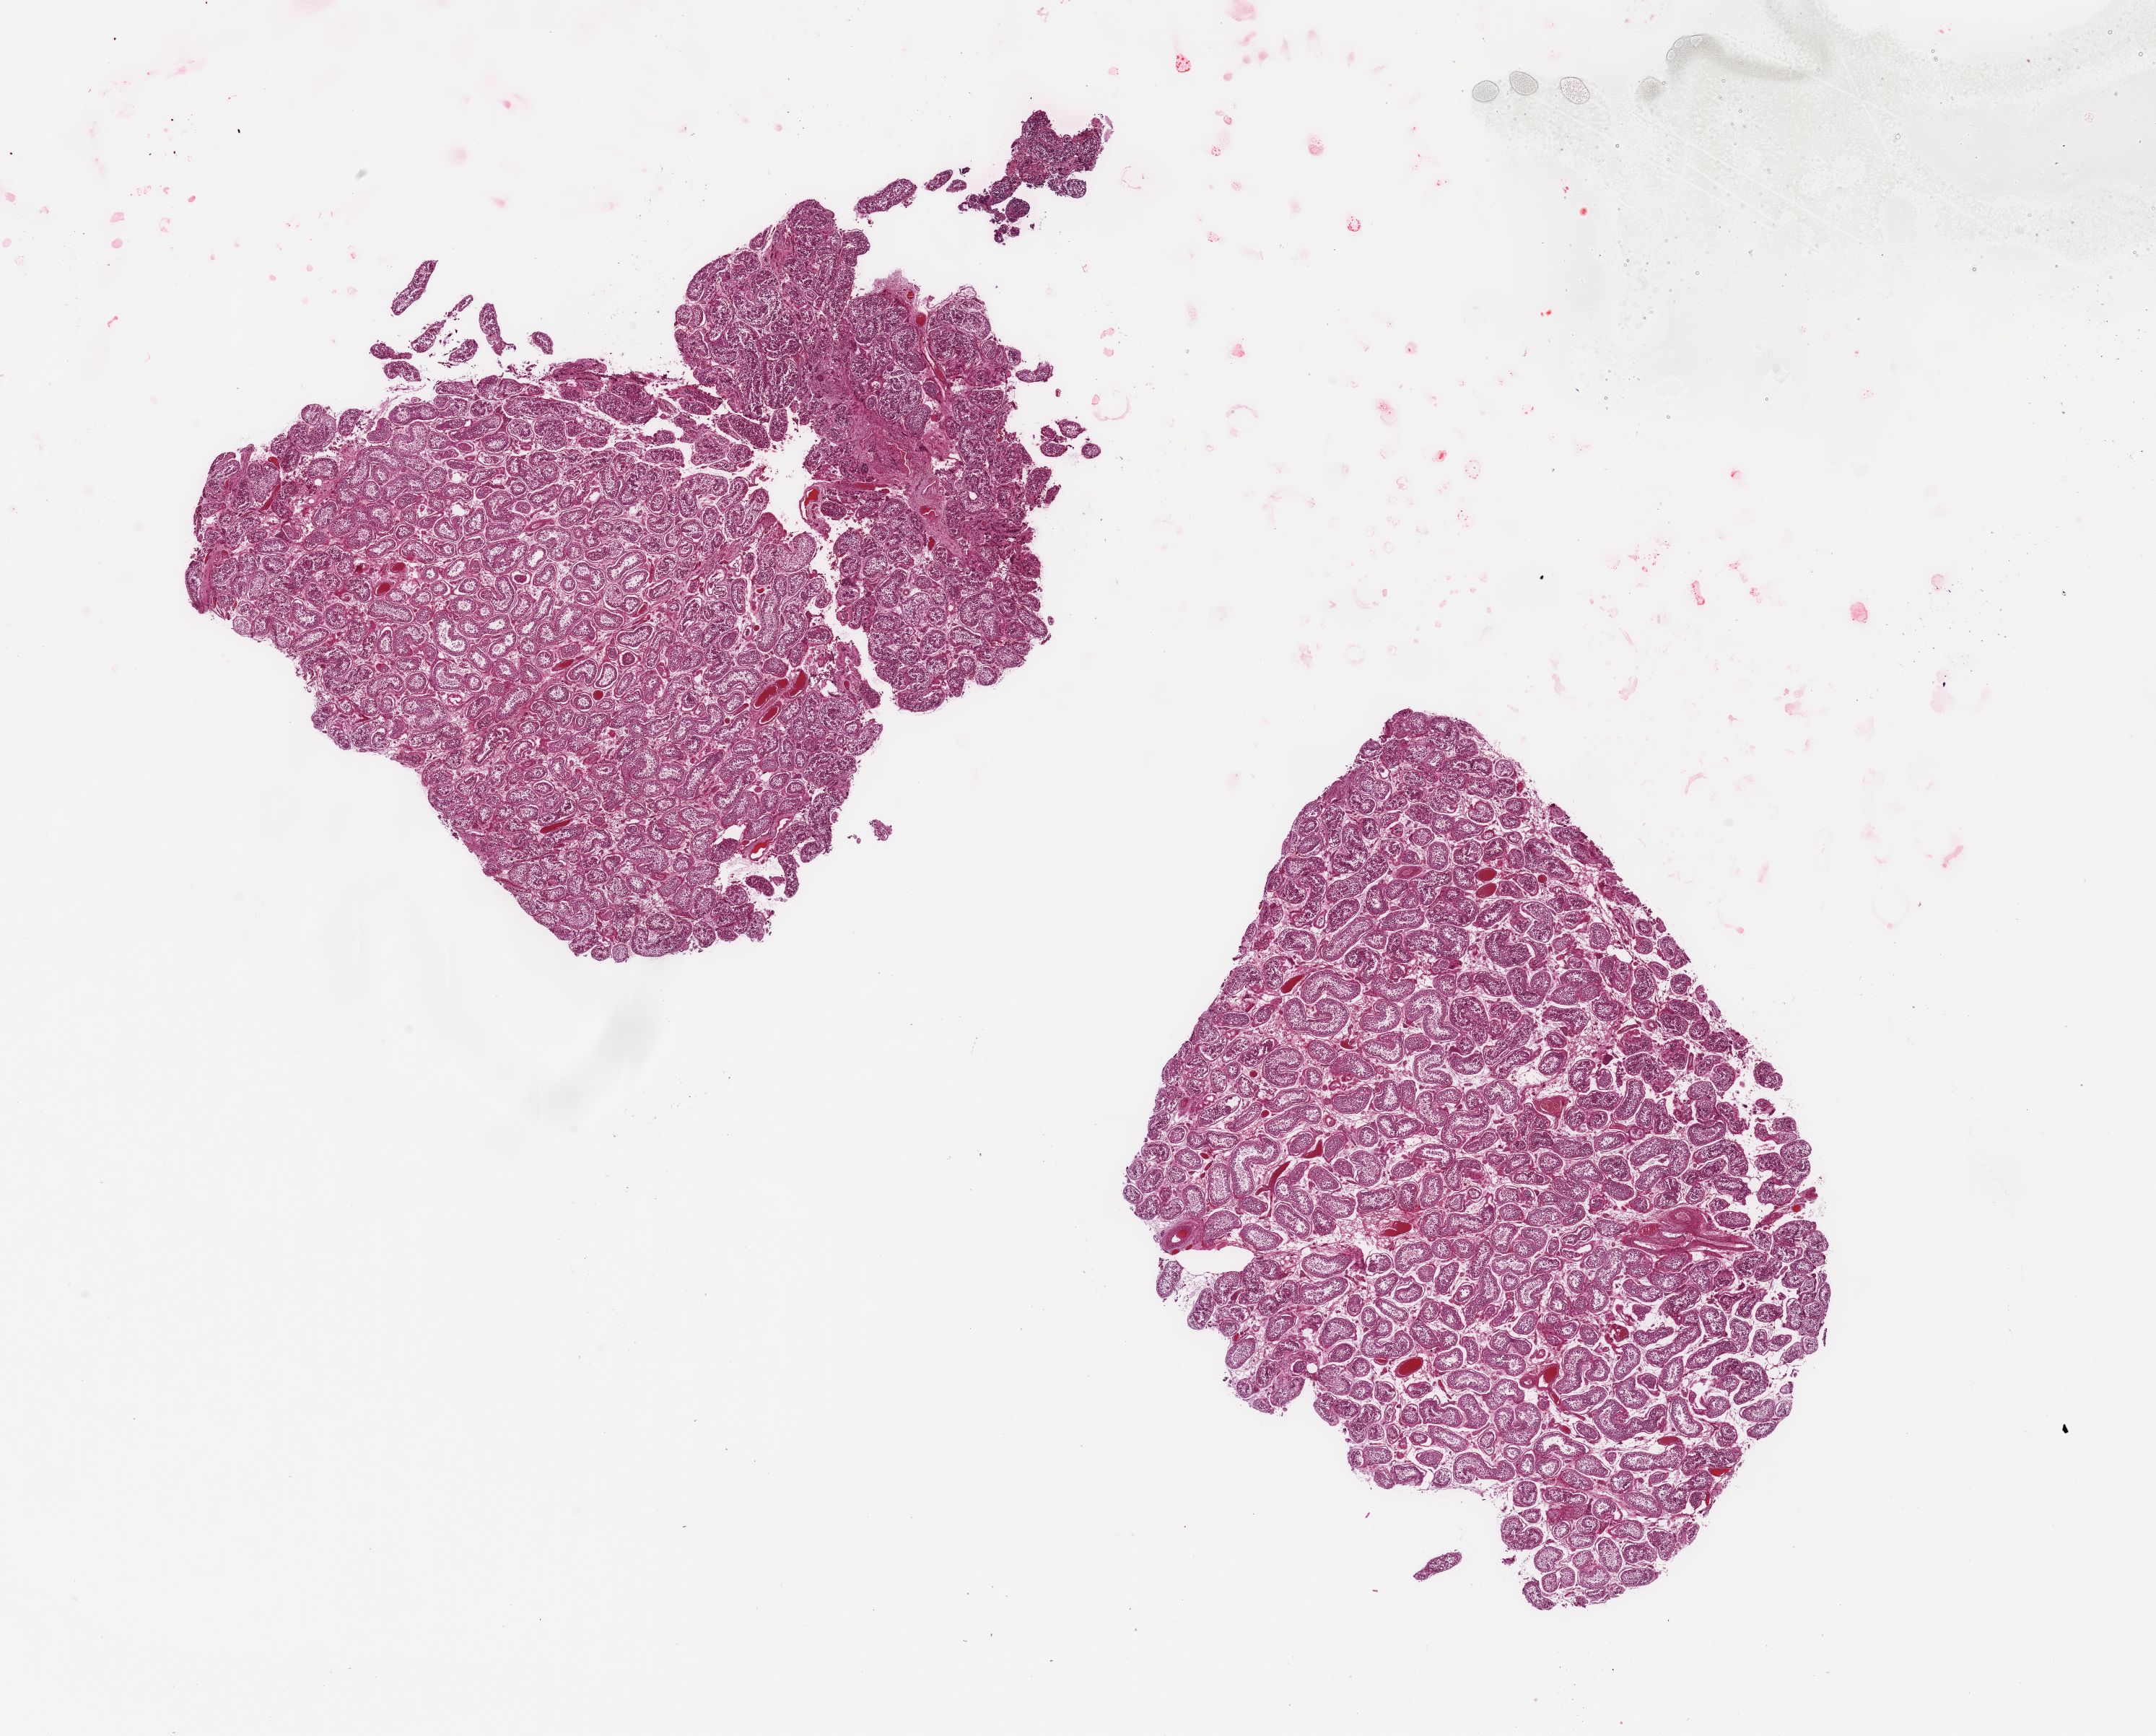
Digitized haematoxylin and eosin-stained section, brightfield — low-resolution overview of the scanned area, about 23.6 x 19.0 mm. PAXgene-fixed paraffin-embedded (PFPE) section. Section of testis (target tissue). Donor tissue sample.
Reviewer comment on this tissue sample: 2 piececs,~8x6mm; spermatogenesis.